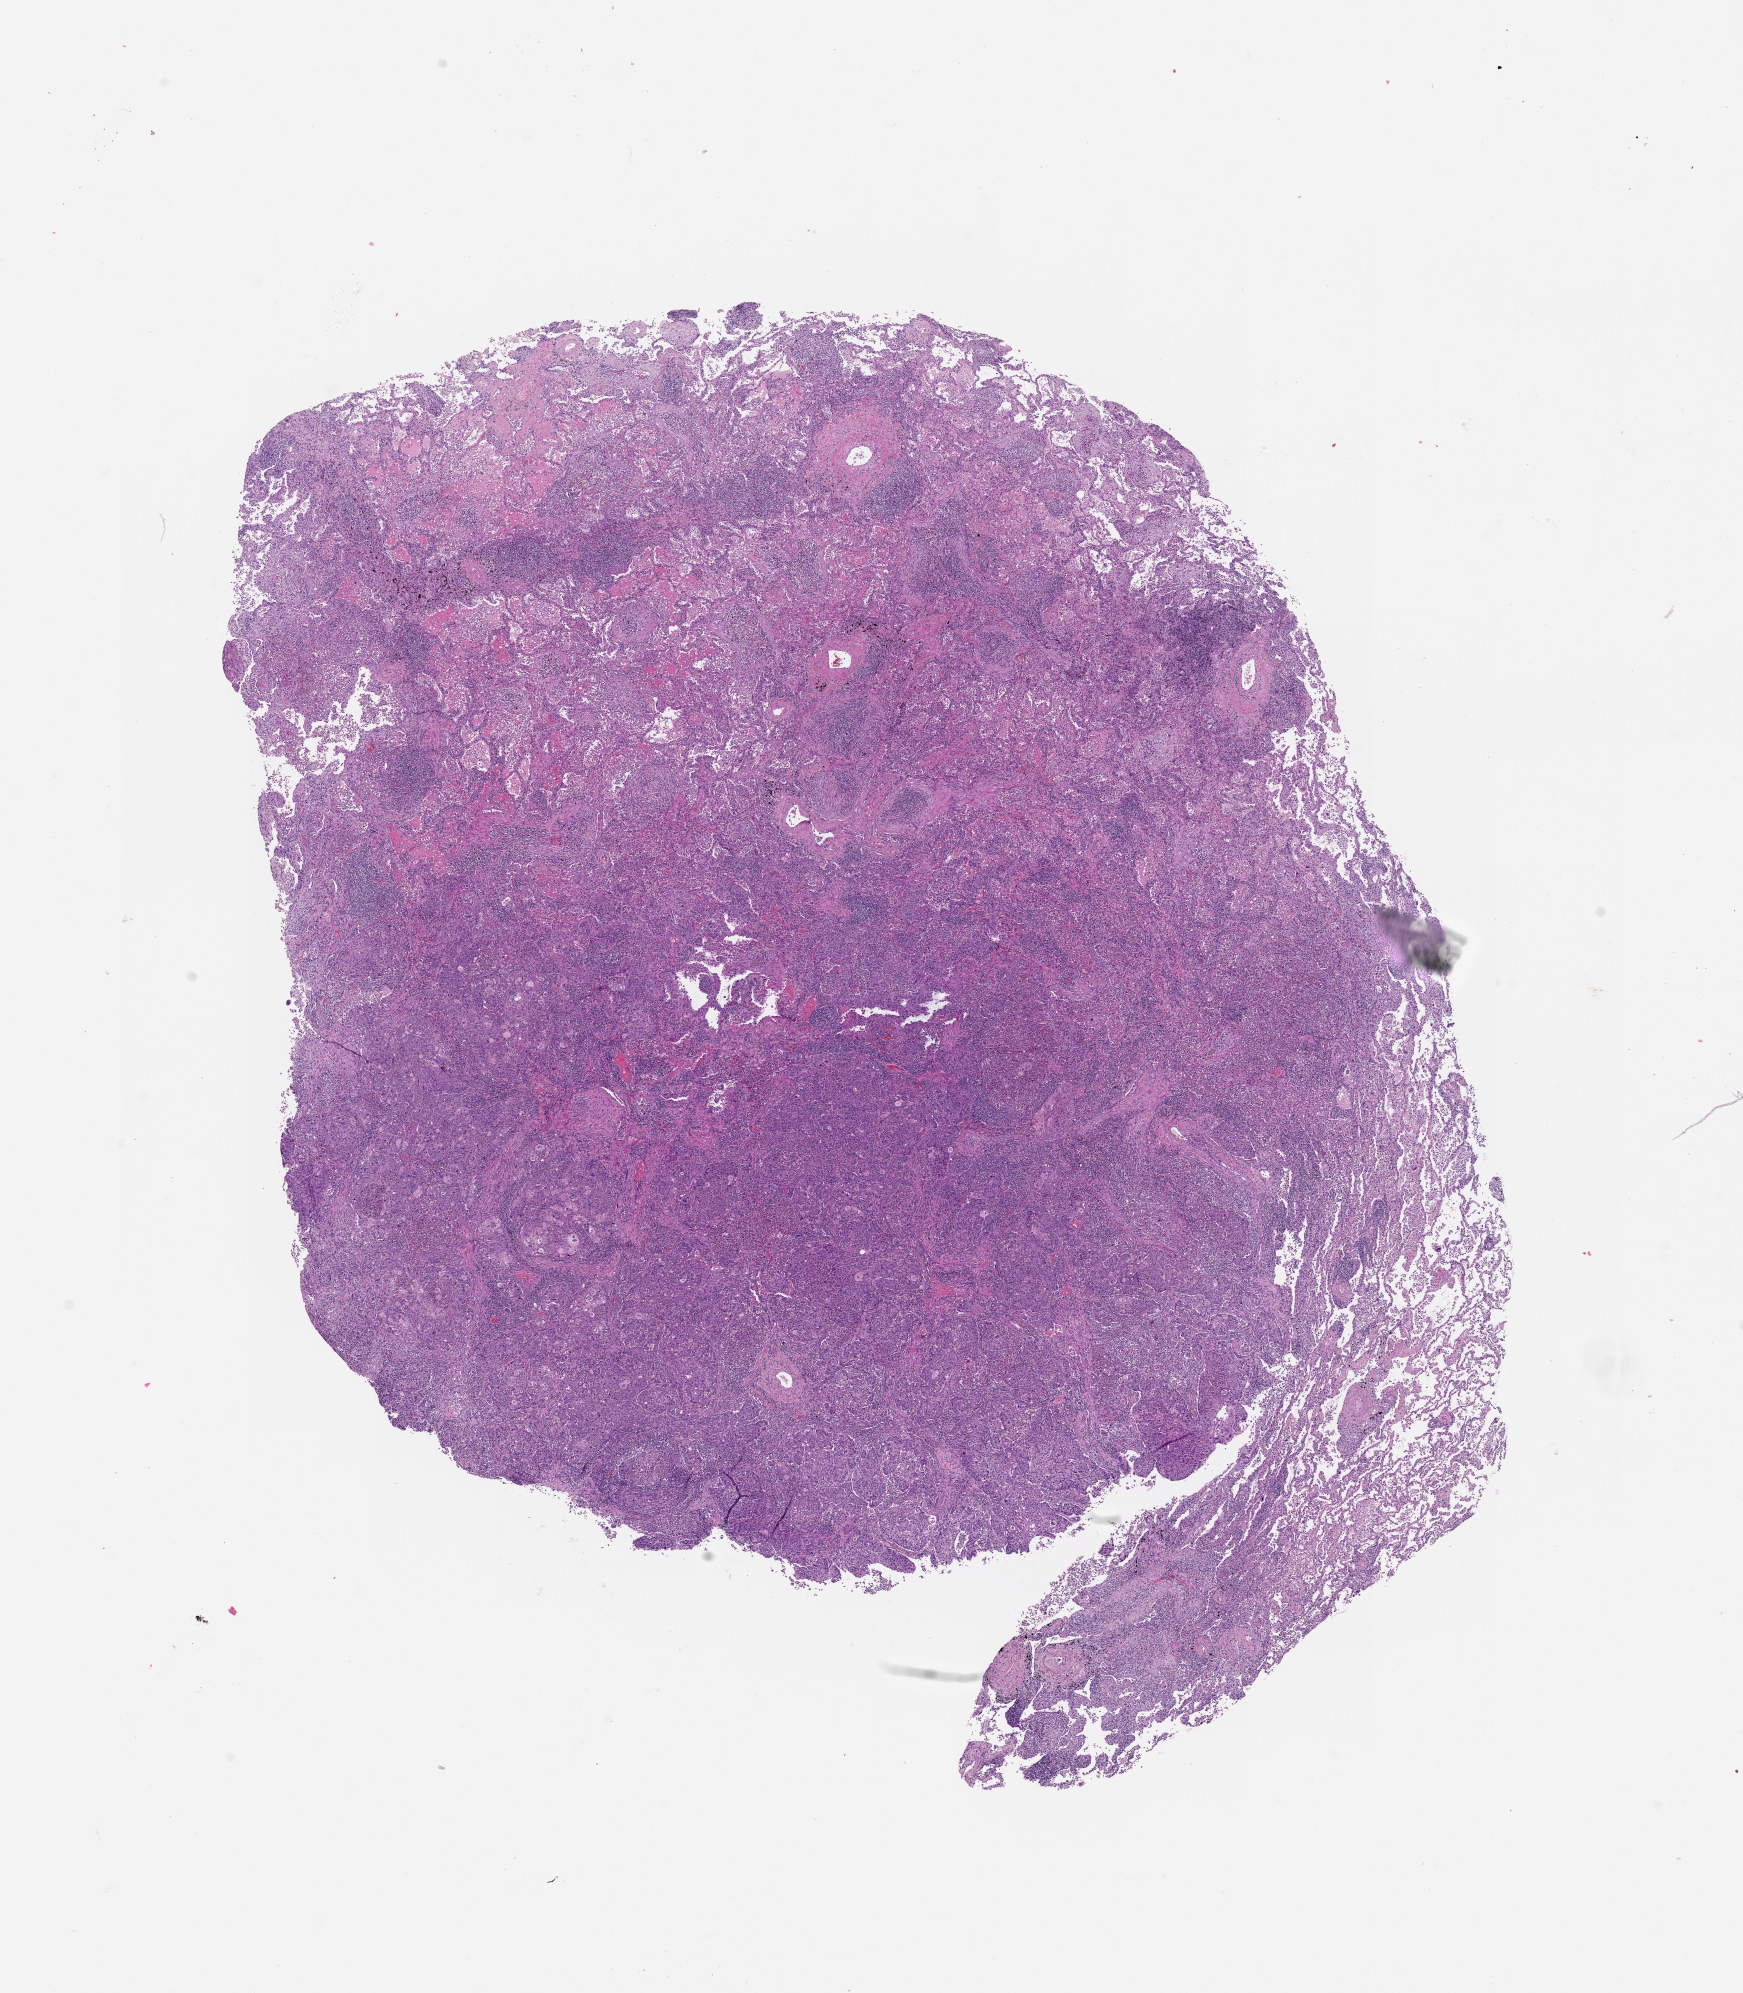
H&E-stained whole-slide image — a low-resolution overview of the entire scanned area, about 14.0 x 16.0 mm. Tumour tissue sample, lung. Patient: male, age 64 years.
Patient diagnosis (cohort enrolment): squamous cell carcinoma (lung).